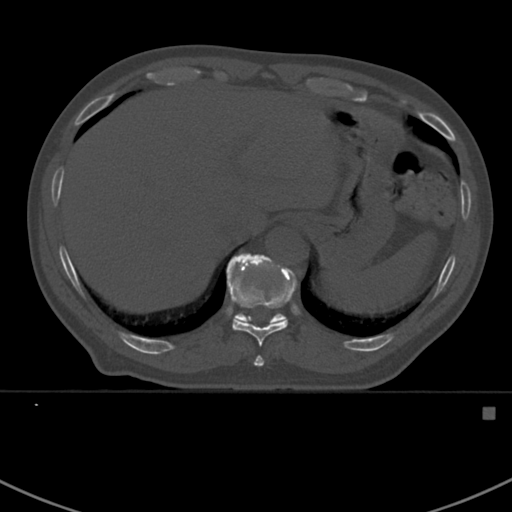
CT including the spine, one axial slice; reconstruction kernel Br40s; bone window (W 1800 / L 400 HU); 512 × 512 image matrix, field of view 358 × 358 mm. Male patient, age 59 years. Case-level facts recorded for this patient, not image findings: primary cancer: prostate.
Outlined on this slice (semi-automatic segmentation, software-assisted and operator-edited):
- T10 vertebra: bounding box (x1, y1, x2, y2) in pixels: (227, 268, 294, 367)
- T11 vertebra: (227, 254, 297, 323)
- T9 vertebra: (257, 356, 259, 359)